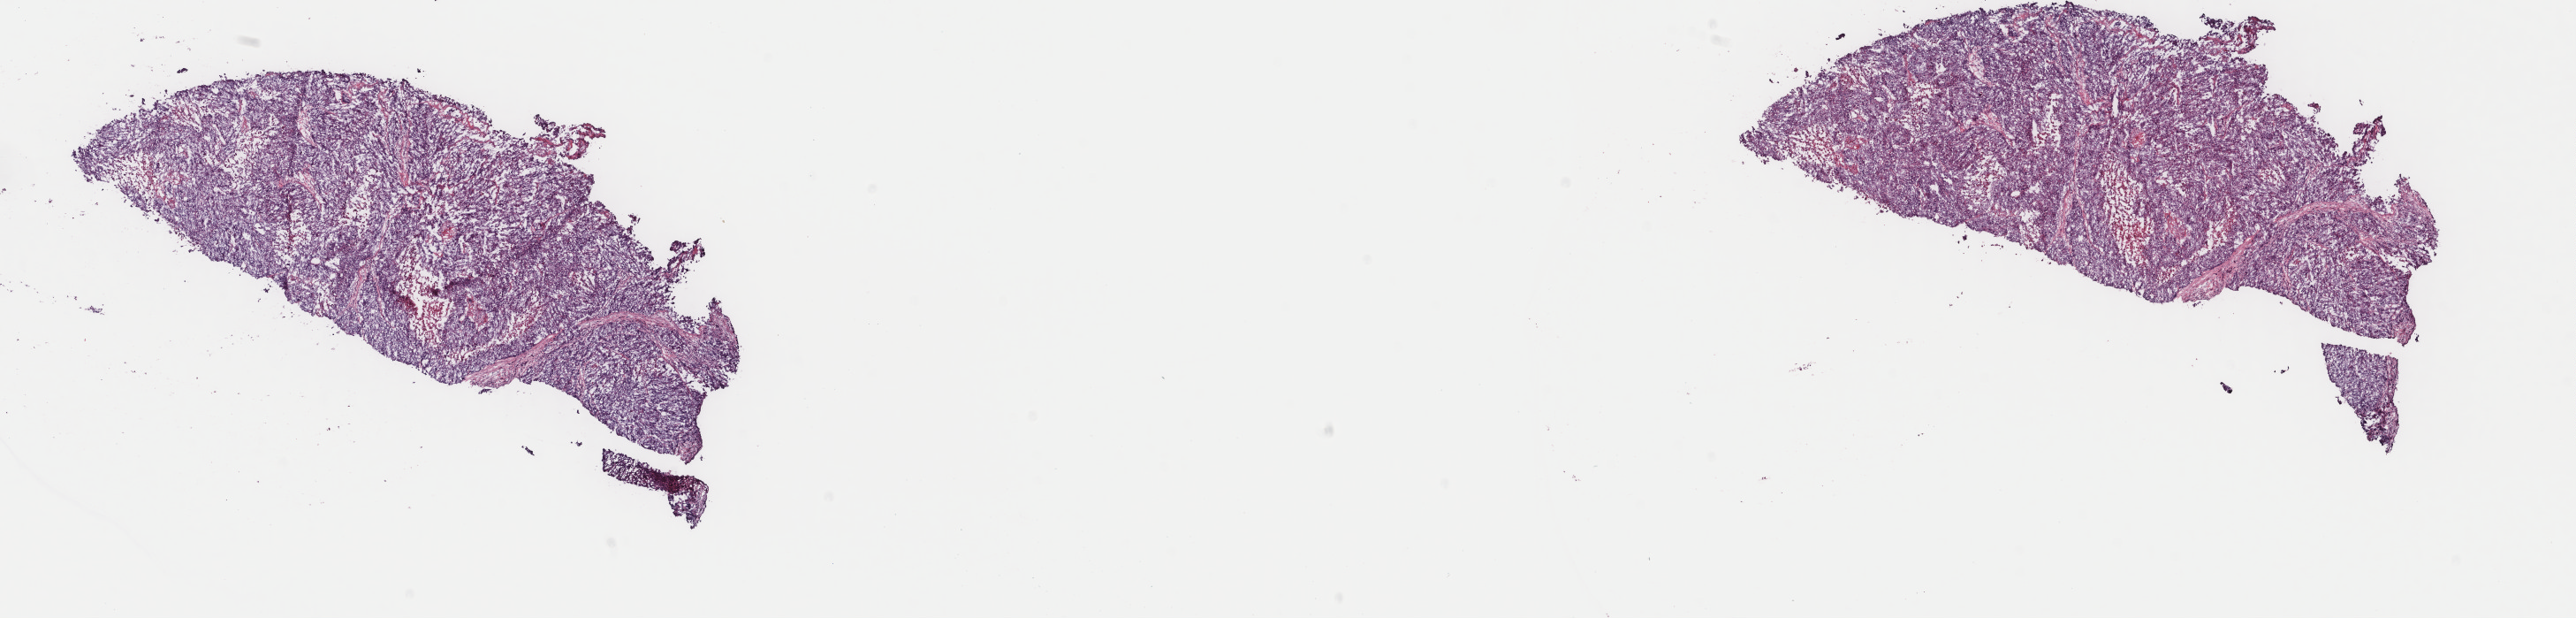
Whole-slide histology image, Hematoxylin and eosin (H&E) stained, shown as a low-resolution overview of the whole scanned area (about 23.1 x 5.5 mm, from a 40x scan), frozen section from the top of the tissue portion, liver, primary tumour sample. Male, age 78 years at initial diagnosis. Histologic grade: G2 (moderately differentiated). Composition of this section per pathologist review: tumour cells 80%, tumour nuclei 80%, normal cells 0%, stromal cells 15%, necrosis 5%. Inflammatory infiltration, as recorded: lymphocyte infiltration 2%, monocyte infiltration 1%, neutrophil infiltration 1%.
TNM: T3 NX M0. Pathologic diagnosis: Hepatocellular carcinoma, NOS. AJCC pathologic stage: IIIA.